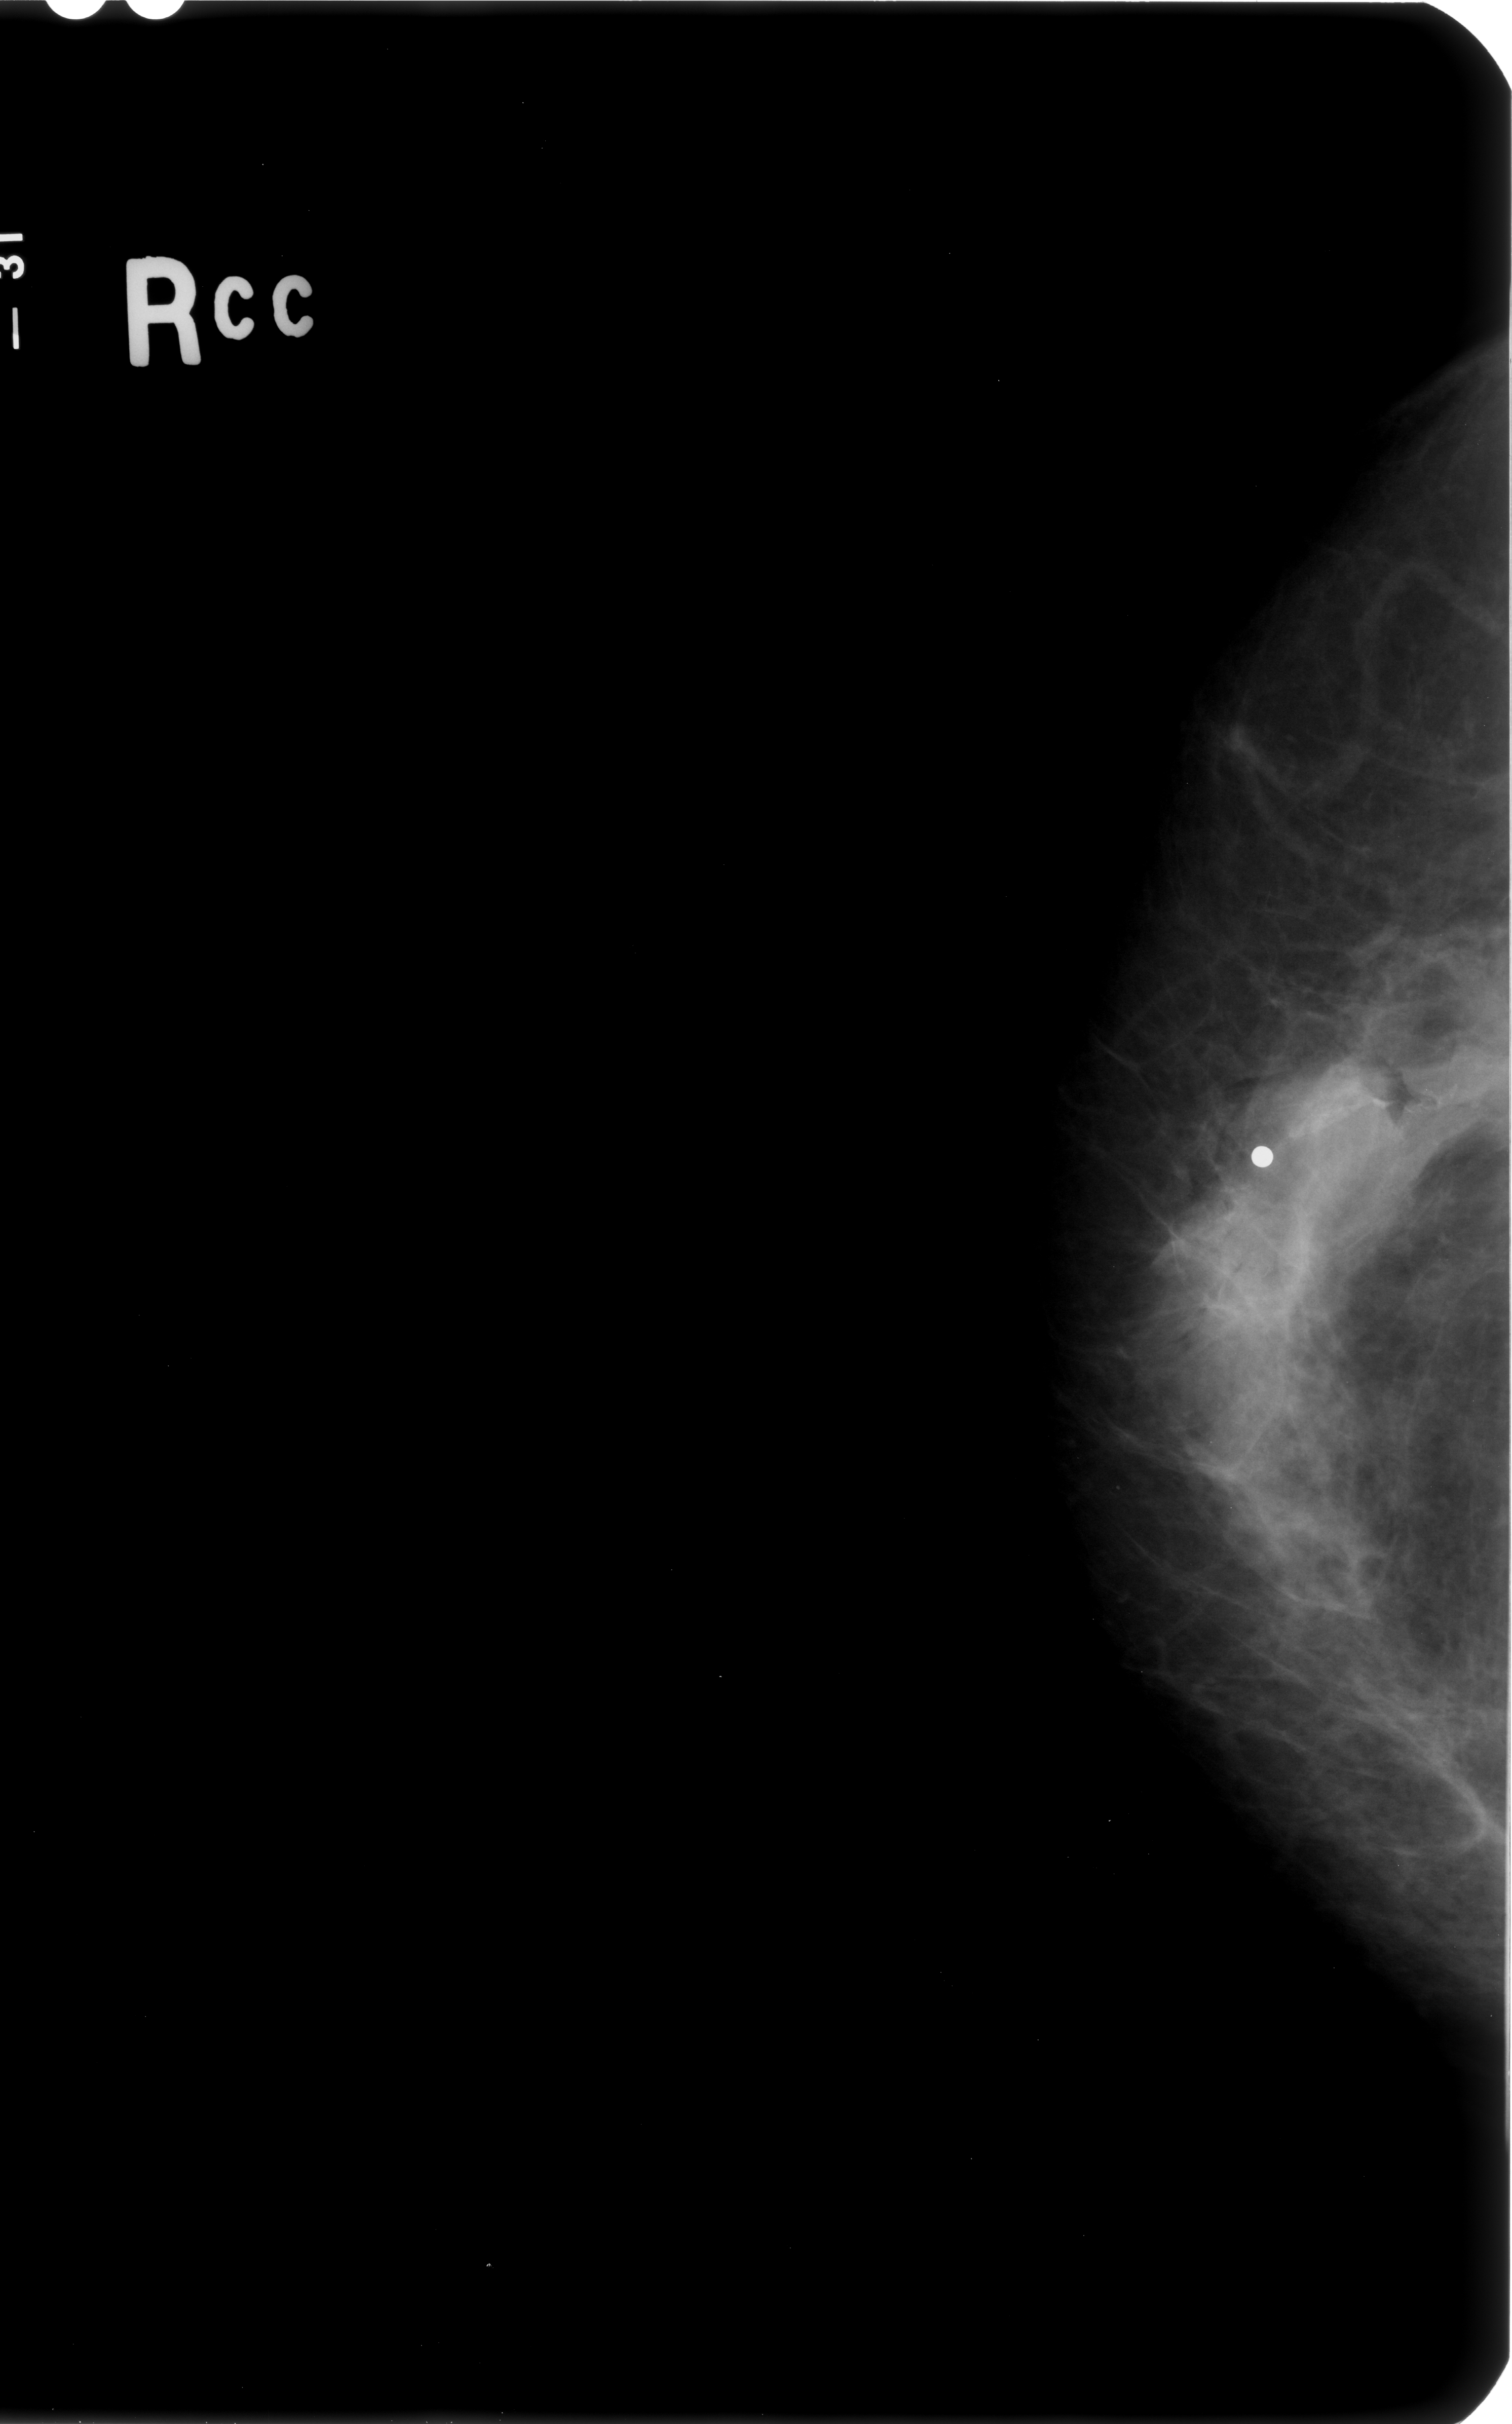
Scanned film-screen mammogram. Right breast. CC view. Breast composition: scattered fibroglandular densities (BI-RADS density category 2 of 4). 1512 × 2424 image matrix.
Expert-marked regions of interest on this film, with their recorded descriptors:
- calcifications, morphology fine linear branching, distribution linear; BI-RADS assessment category 4; subtlety rating 5 on a 1 (subtle) to 5 (obvious) scale; pathology result (as recorded, not read from the image): malignant: bounding box (x1, y1, x2, y2) in pixels: (1191, 1033, 1509, 1363)